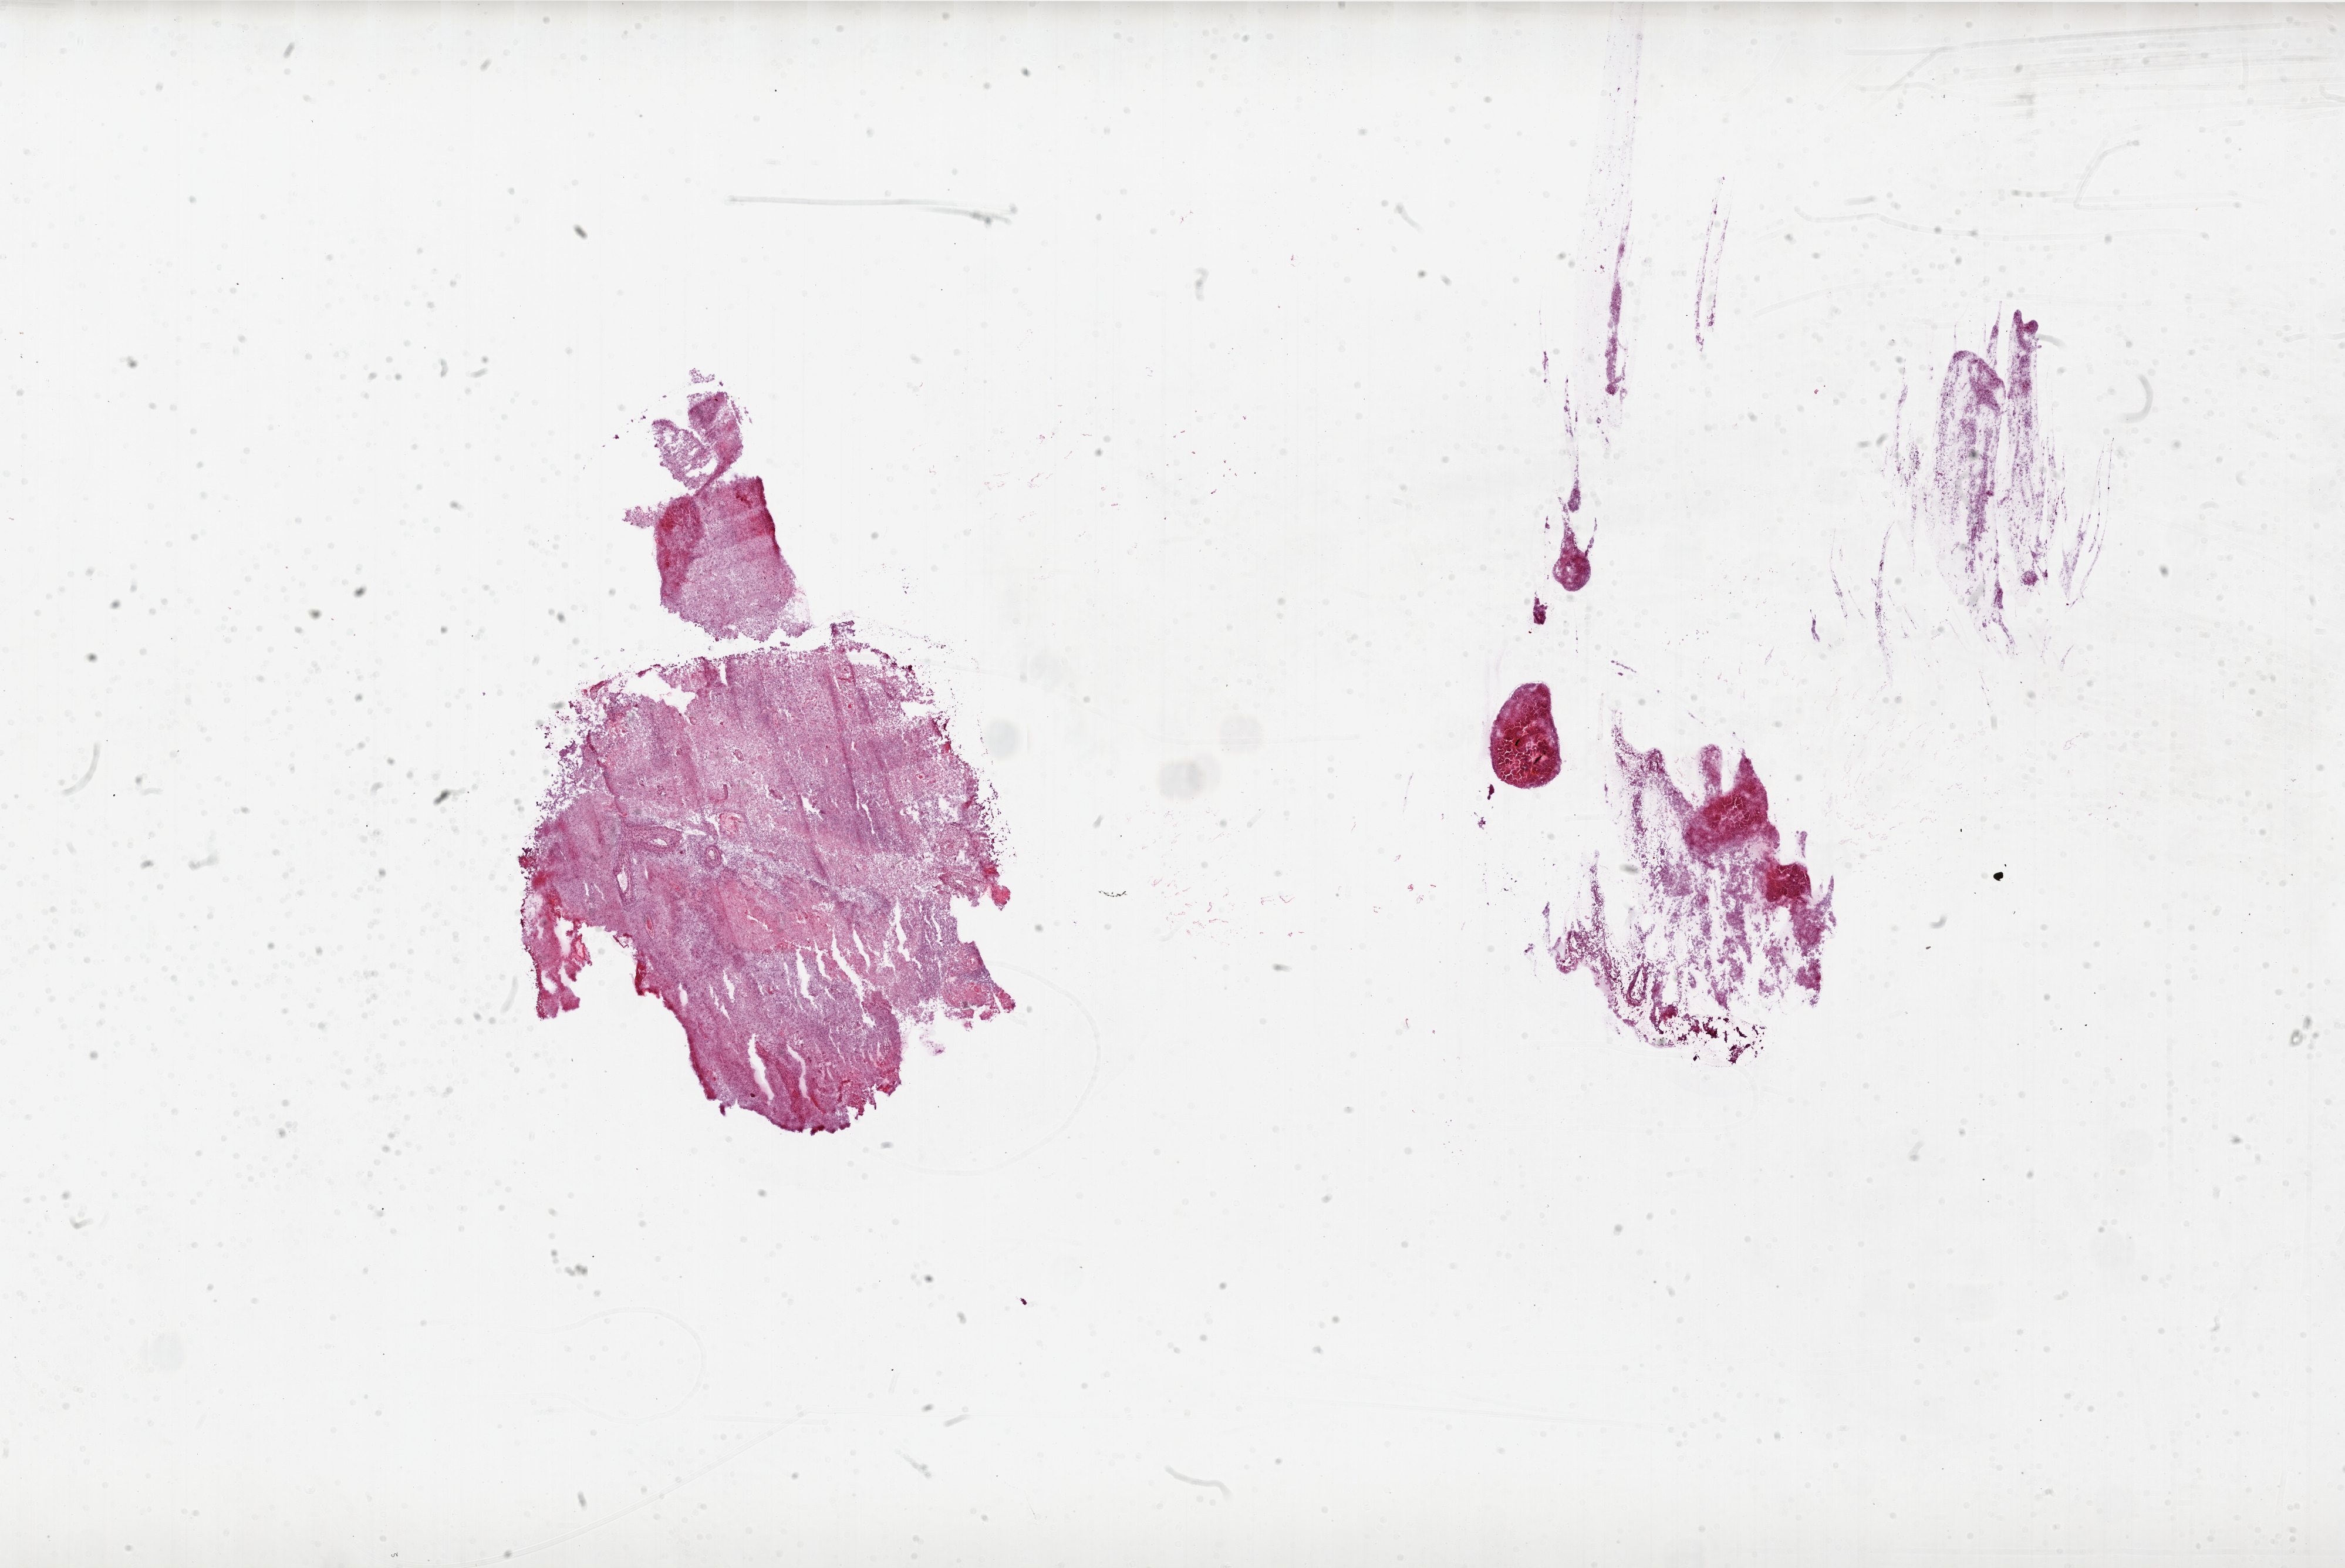
Digitized H&E-stained tissue section (whole slide) — whole scanned area (about 32.0 x 21.4 mm) shown as a low-resolution overview. Frozen section from the bottom of the tissue portion. Brain, primary tumour sample. Female, age 81 years at initial diagnosis. Pathologist review of this section (percent, as recorded): tumour cells 25%, tumour nuclei 75%, normal cells 0%, stromal cells 5%, necrosis 70%. Infiltration values recorded for this section: lymphocyte infiltration 0%, neutrophil infiltration 80%.
Histologic diagnosis: Glioblastoma.